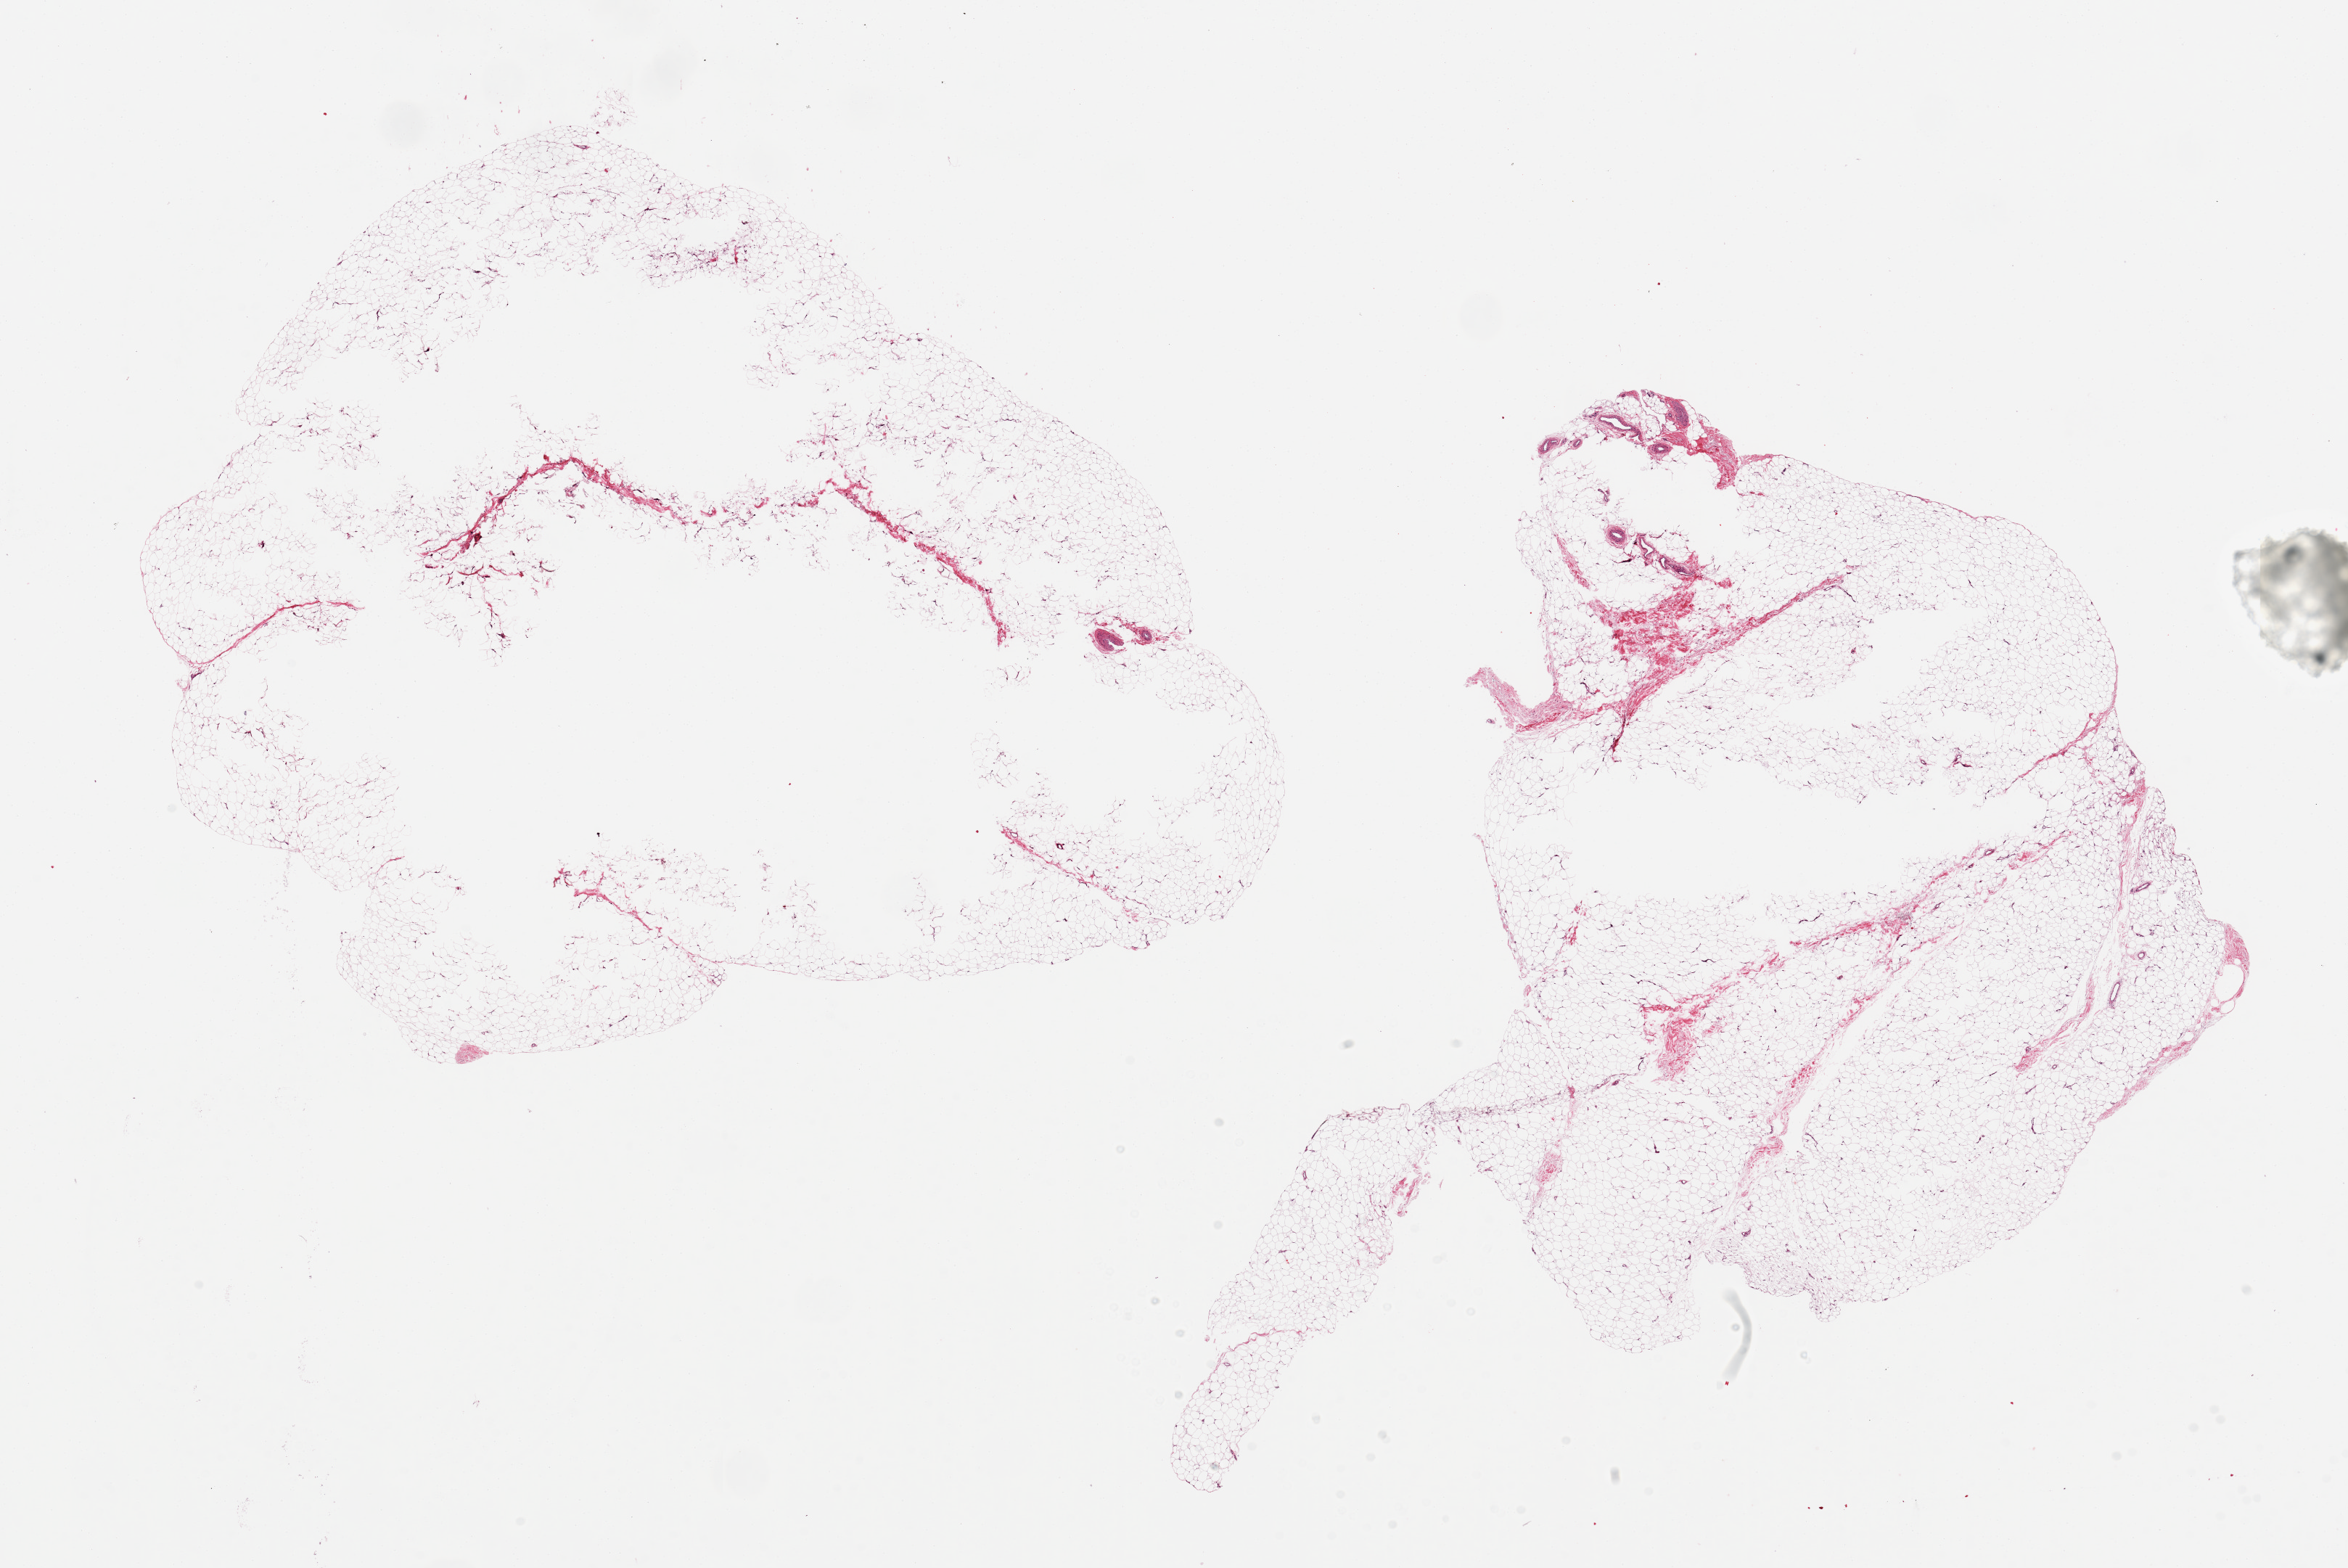
Digitized haematoxylin and eosin-stained section, brightfield — a low-resolution overview of the entire scanned area, about 25.6 x 17.1 mm (from a 20x scan); PAXgene-fixed paraffin-embedded (PFPE) section; section of adipose tissue (target tissue); tissue donor sample. Donor sex: female.
Pathologist's review note for this sample: 2 aliquots, ~9x8mm.